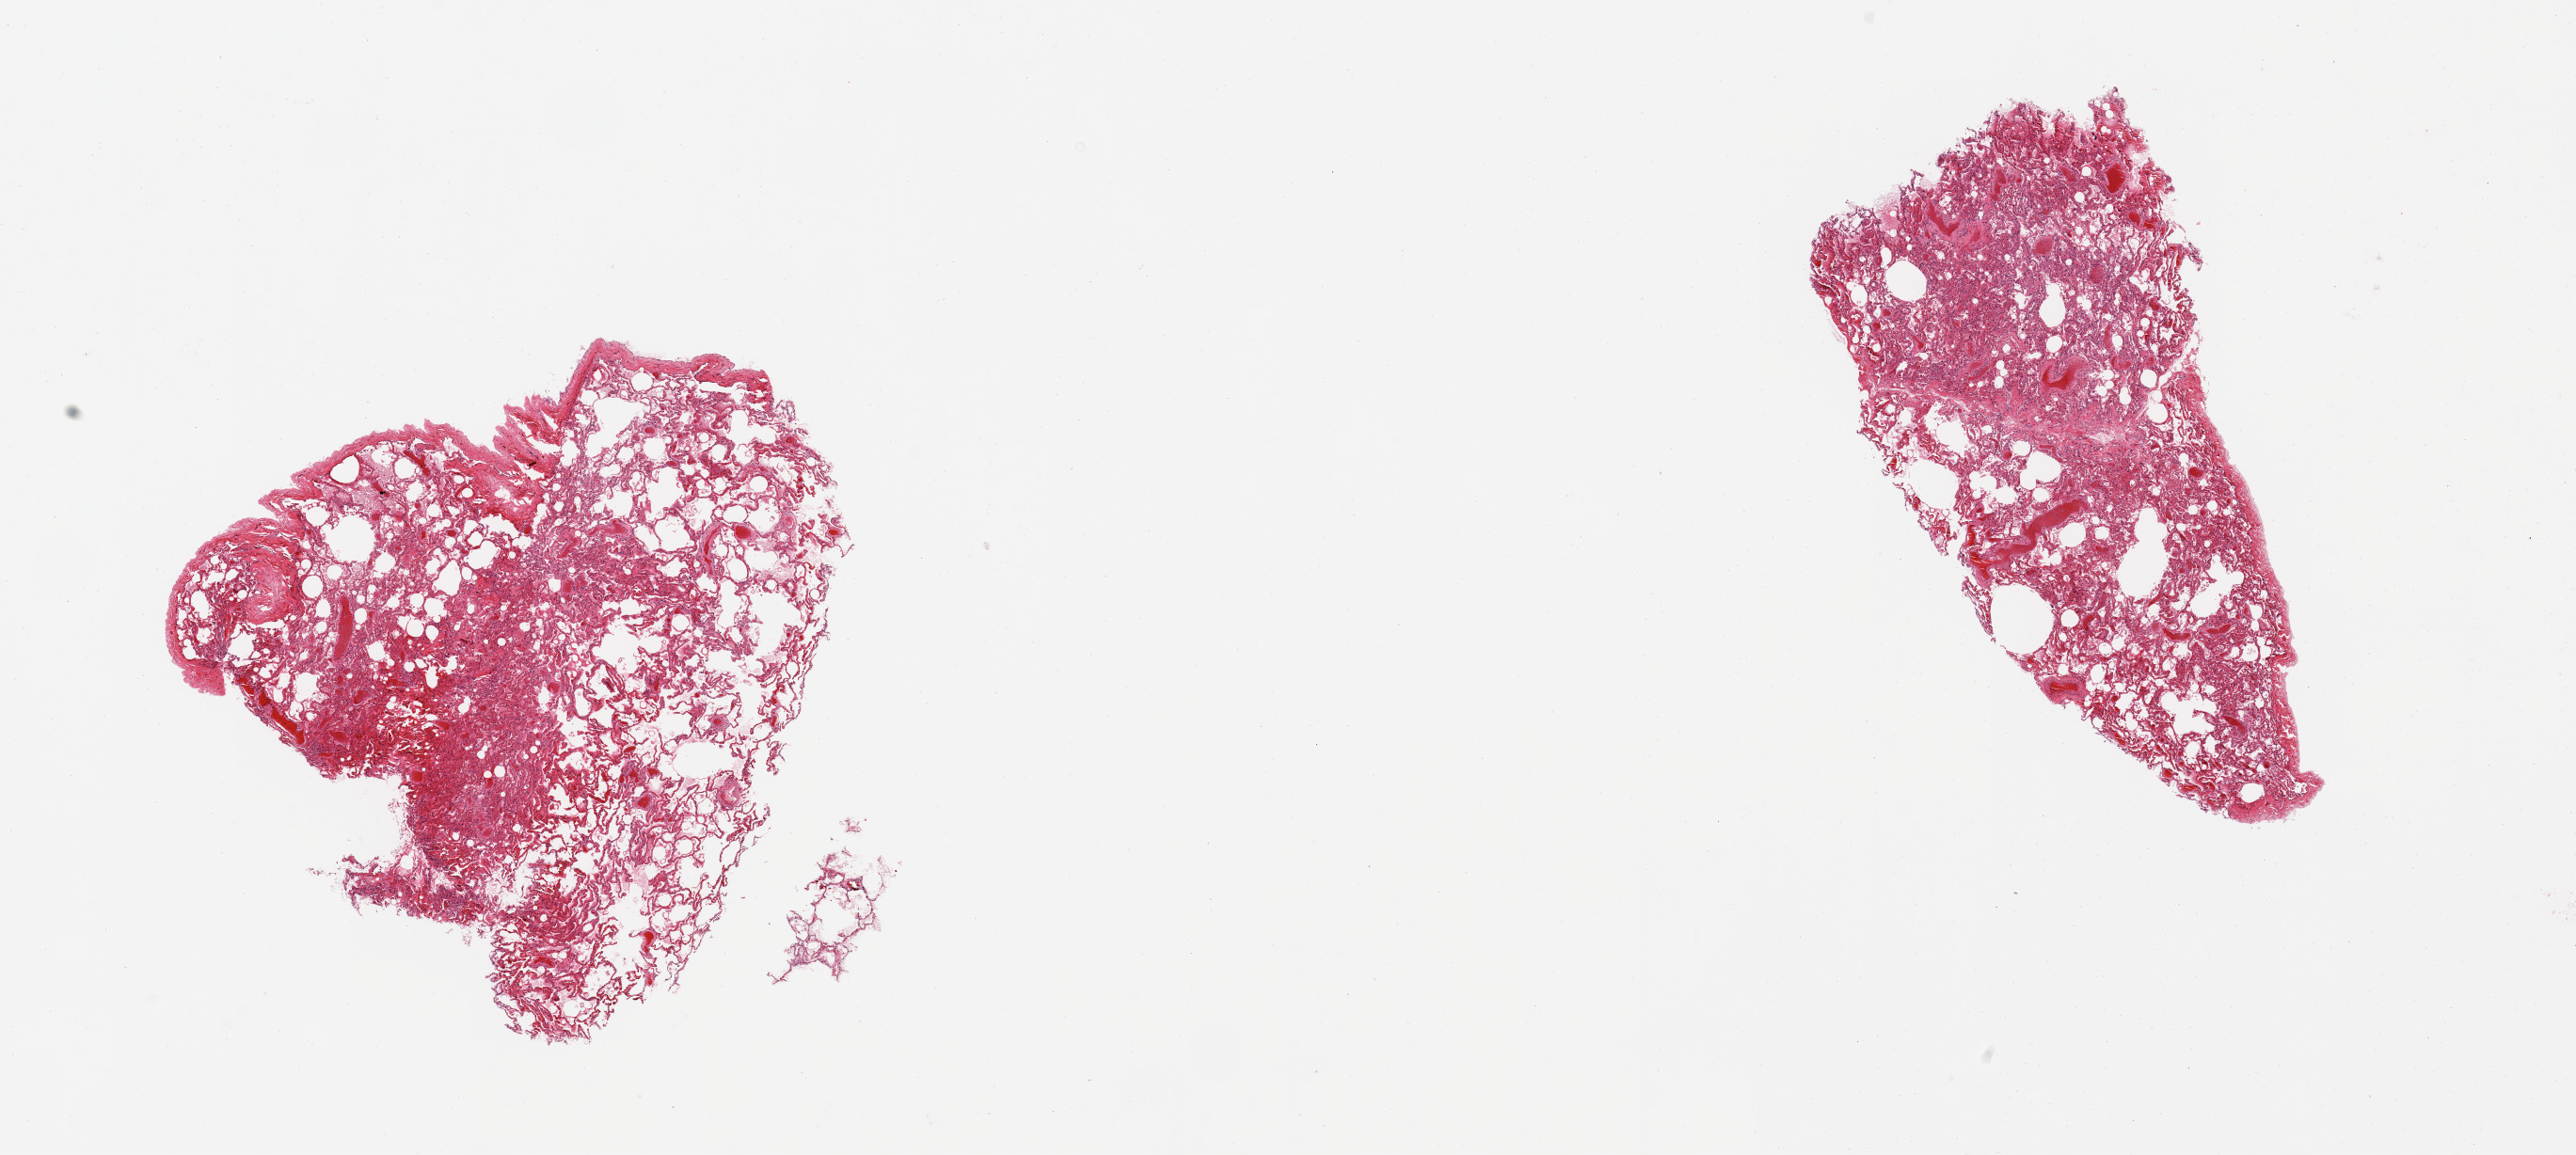
Whole-slide image, H&E stain, a low-resolution overview of the entire scanned area, about 21.7 x 9.7 mm (acquisition: 20x scan); PAXgene-fixed, paraffin-embedded tissue; sampled site (target tissue): lung; donor tissue sample. Donor sex: male.
Reviewer comment on this tissue sample: 2; moderately congested.